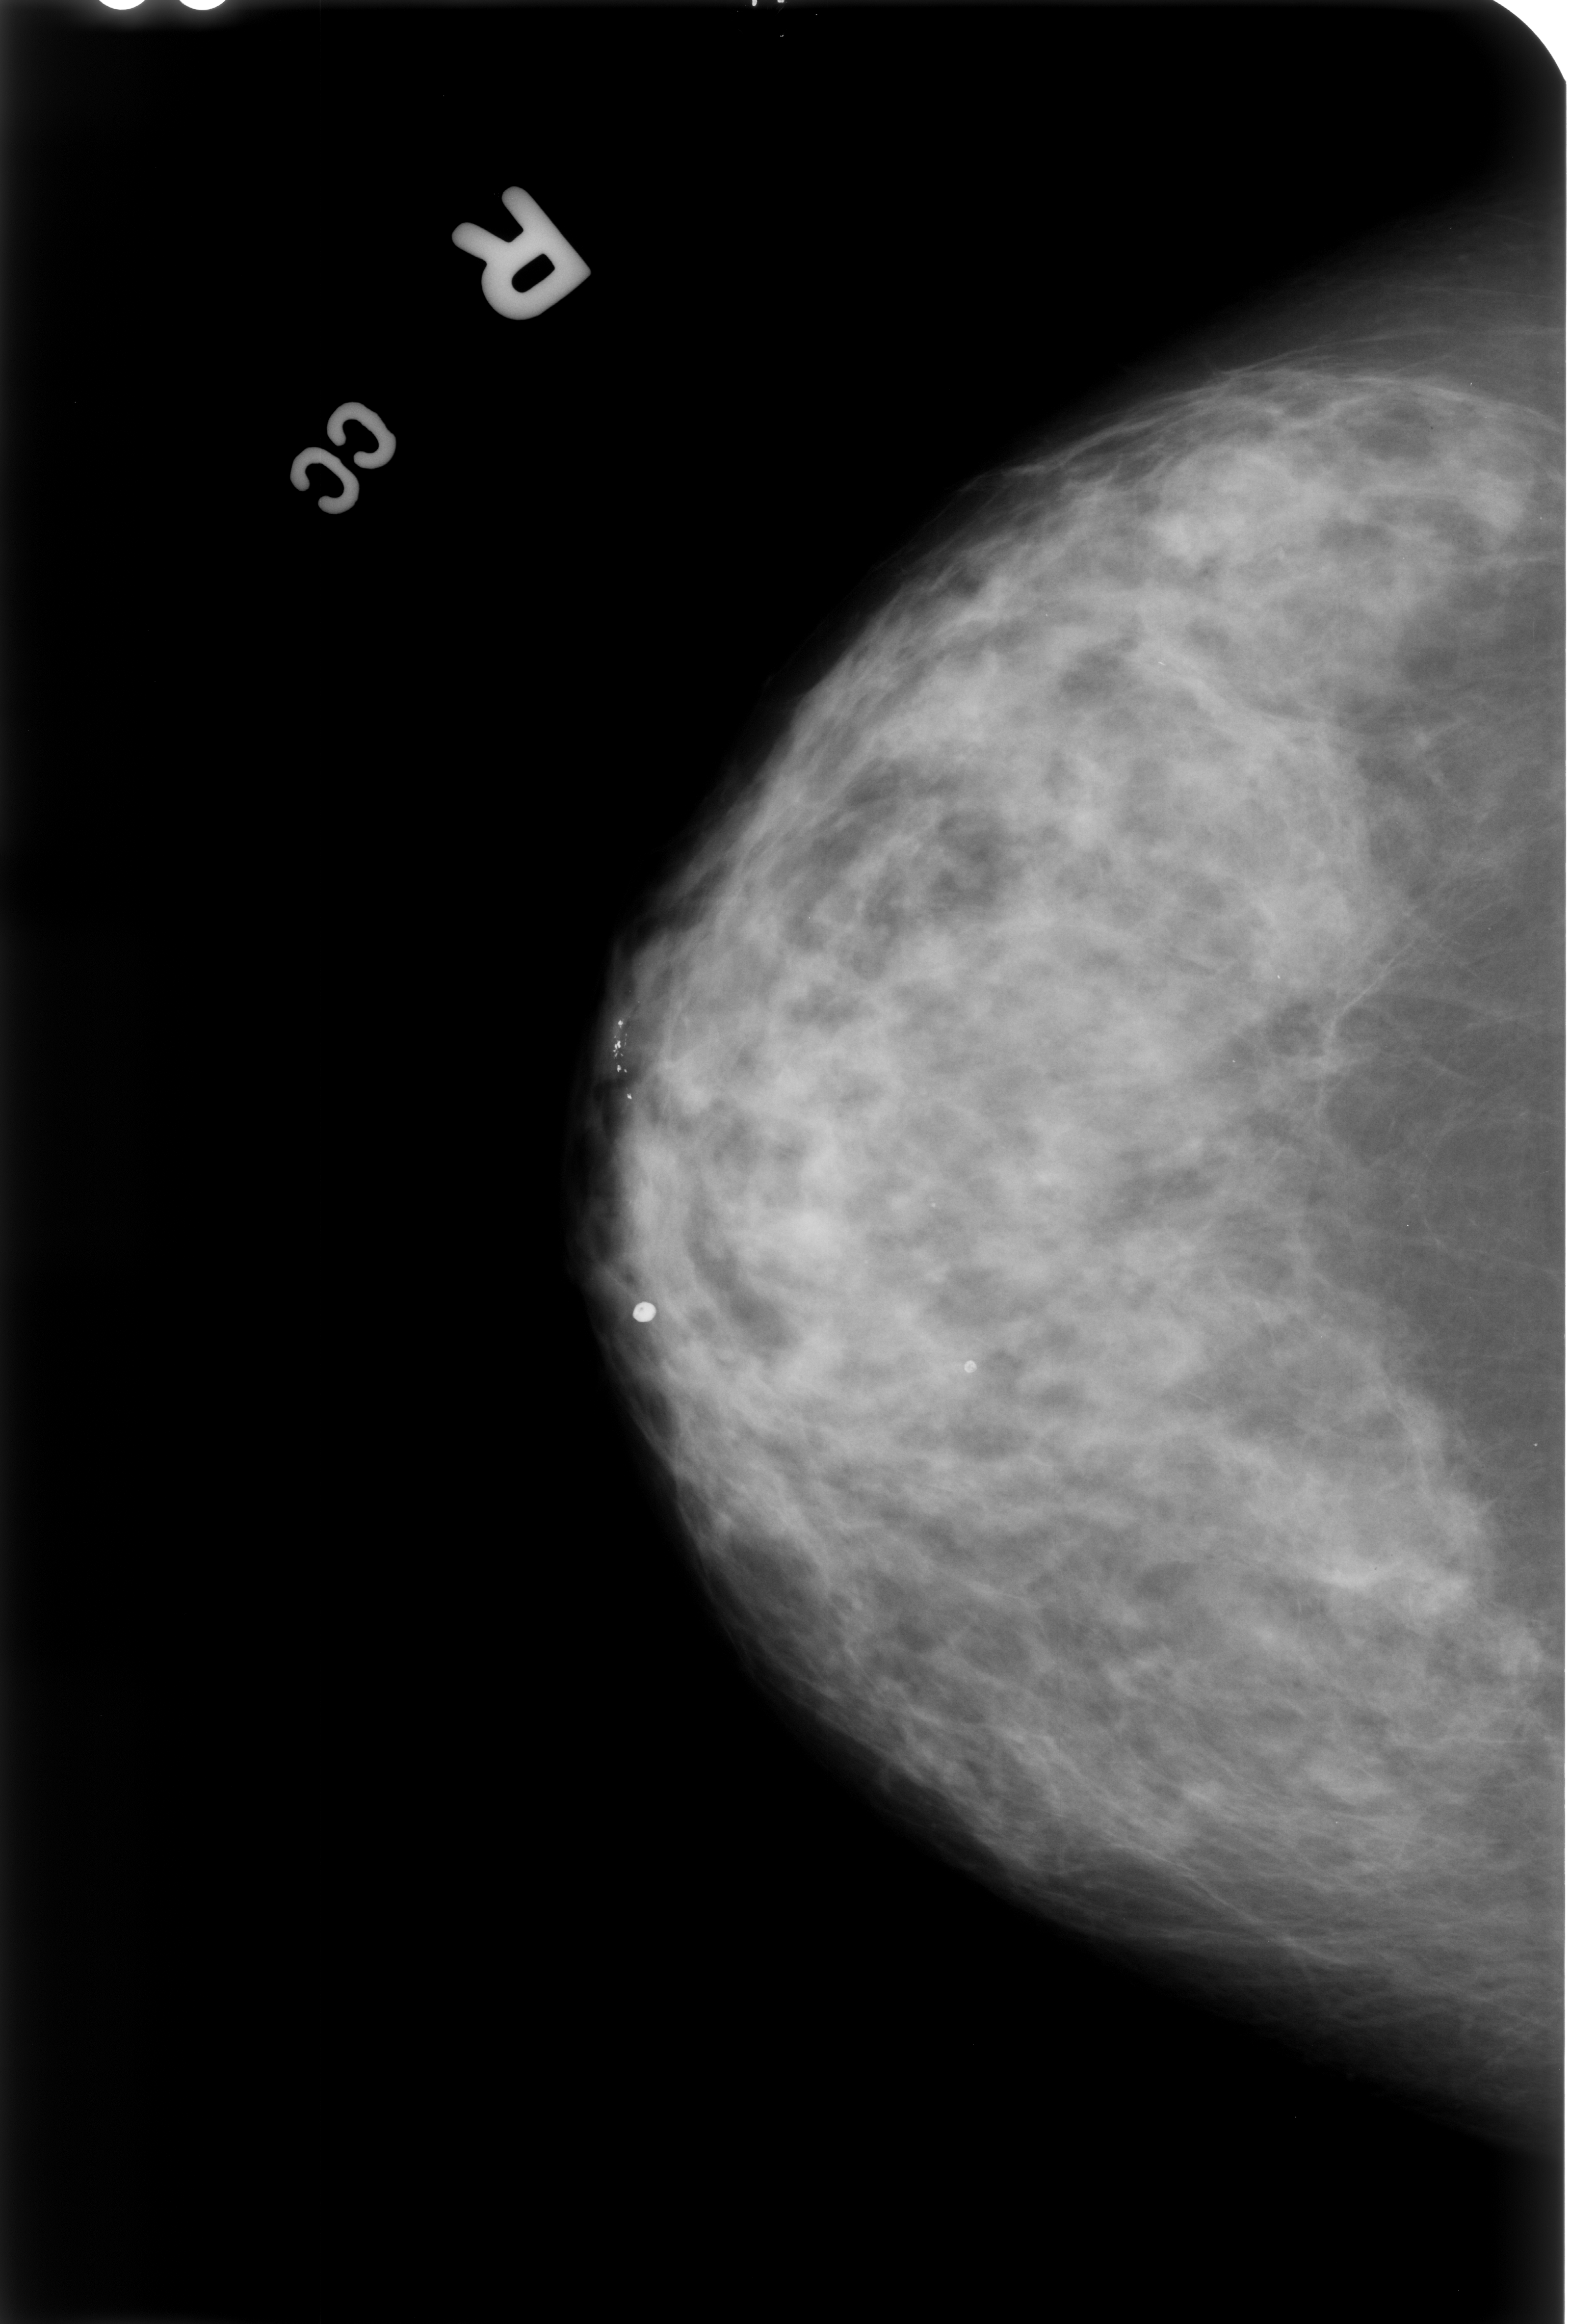
Digitized screen-film mammogram; right breast; craniocaudal (CC) view; breast composition: heterogeneously dense (BI-RADS density category 3 of 4); 1570 × 2324 image matrix.
Marked abnormalities (boxes around the expert regions of interest):
- Finding 1 of 2: calcifications, morphology lucent center; BI-RADS assessment category 2; outcome (as recorded, no biopsy): benign without callback (not worked up further): bounding box [x1, y1, x2, y2] px = [701, 1500, 739, 1546]
- Finding 2 of 2: calcifications, morphology lucent center; BI-RADS assessment category 2; subtlety rating 5 on a 1 (subtle) to 5 (obvious) scale; benign; no additional work-up was recommended (outcome (as recorded, no biopsy): benign without callback): [950, 1349, 984, 1395]